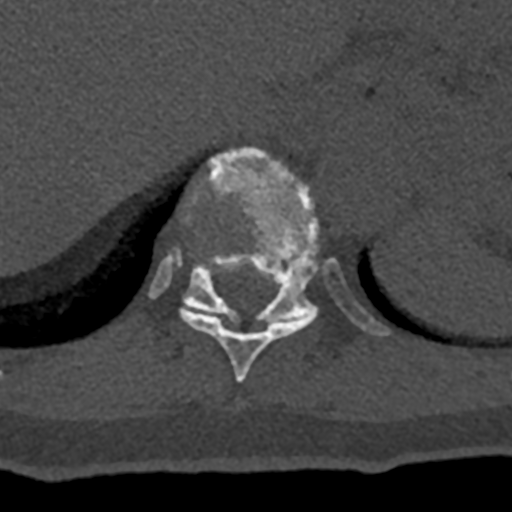
CT including the spine, one axial slice; 120 kVp; bone window (W 1800 / L 400 HU); 0.5 mm slice thickness; 512 × 512 image matrix, field of view 160 × 160 mm. Patient: male, 74 years. From the clinical record (not read from this slice): primary cancer: renal.
Structures marked on this image (semi-automatic segmentation, software-assisted and operator-edited):
- T10 vertebra: box from (x=180, y=268) to (x=315, y=383) px
- T11 vertebra: (x=149, y=147)–(x=390, y=336)